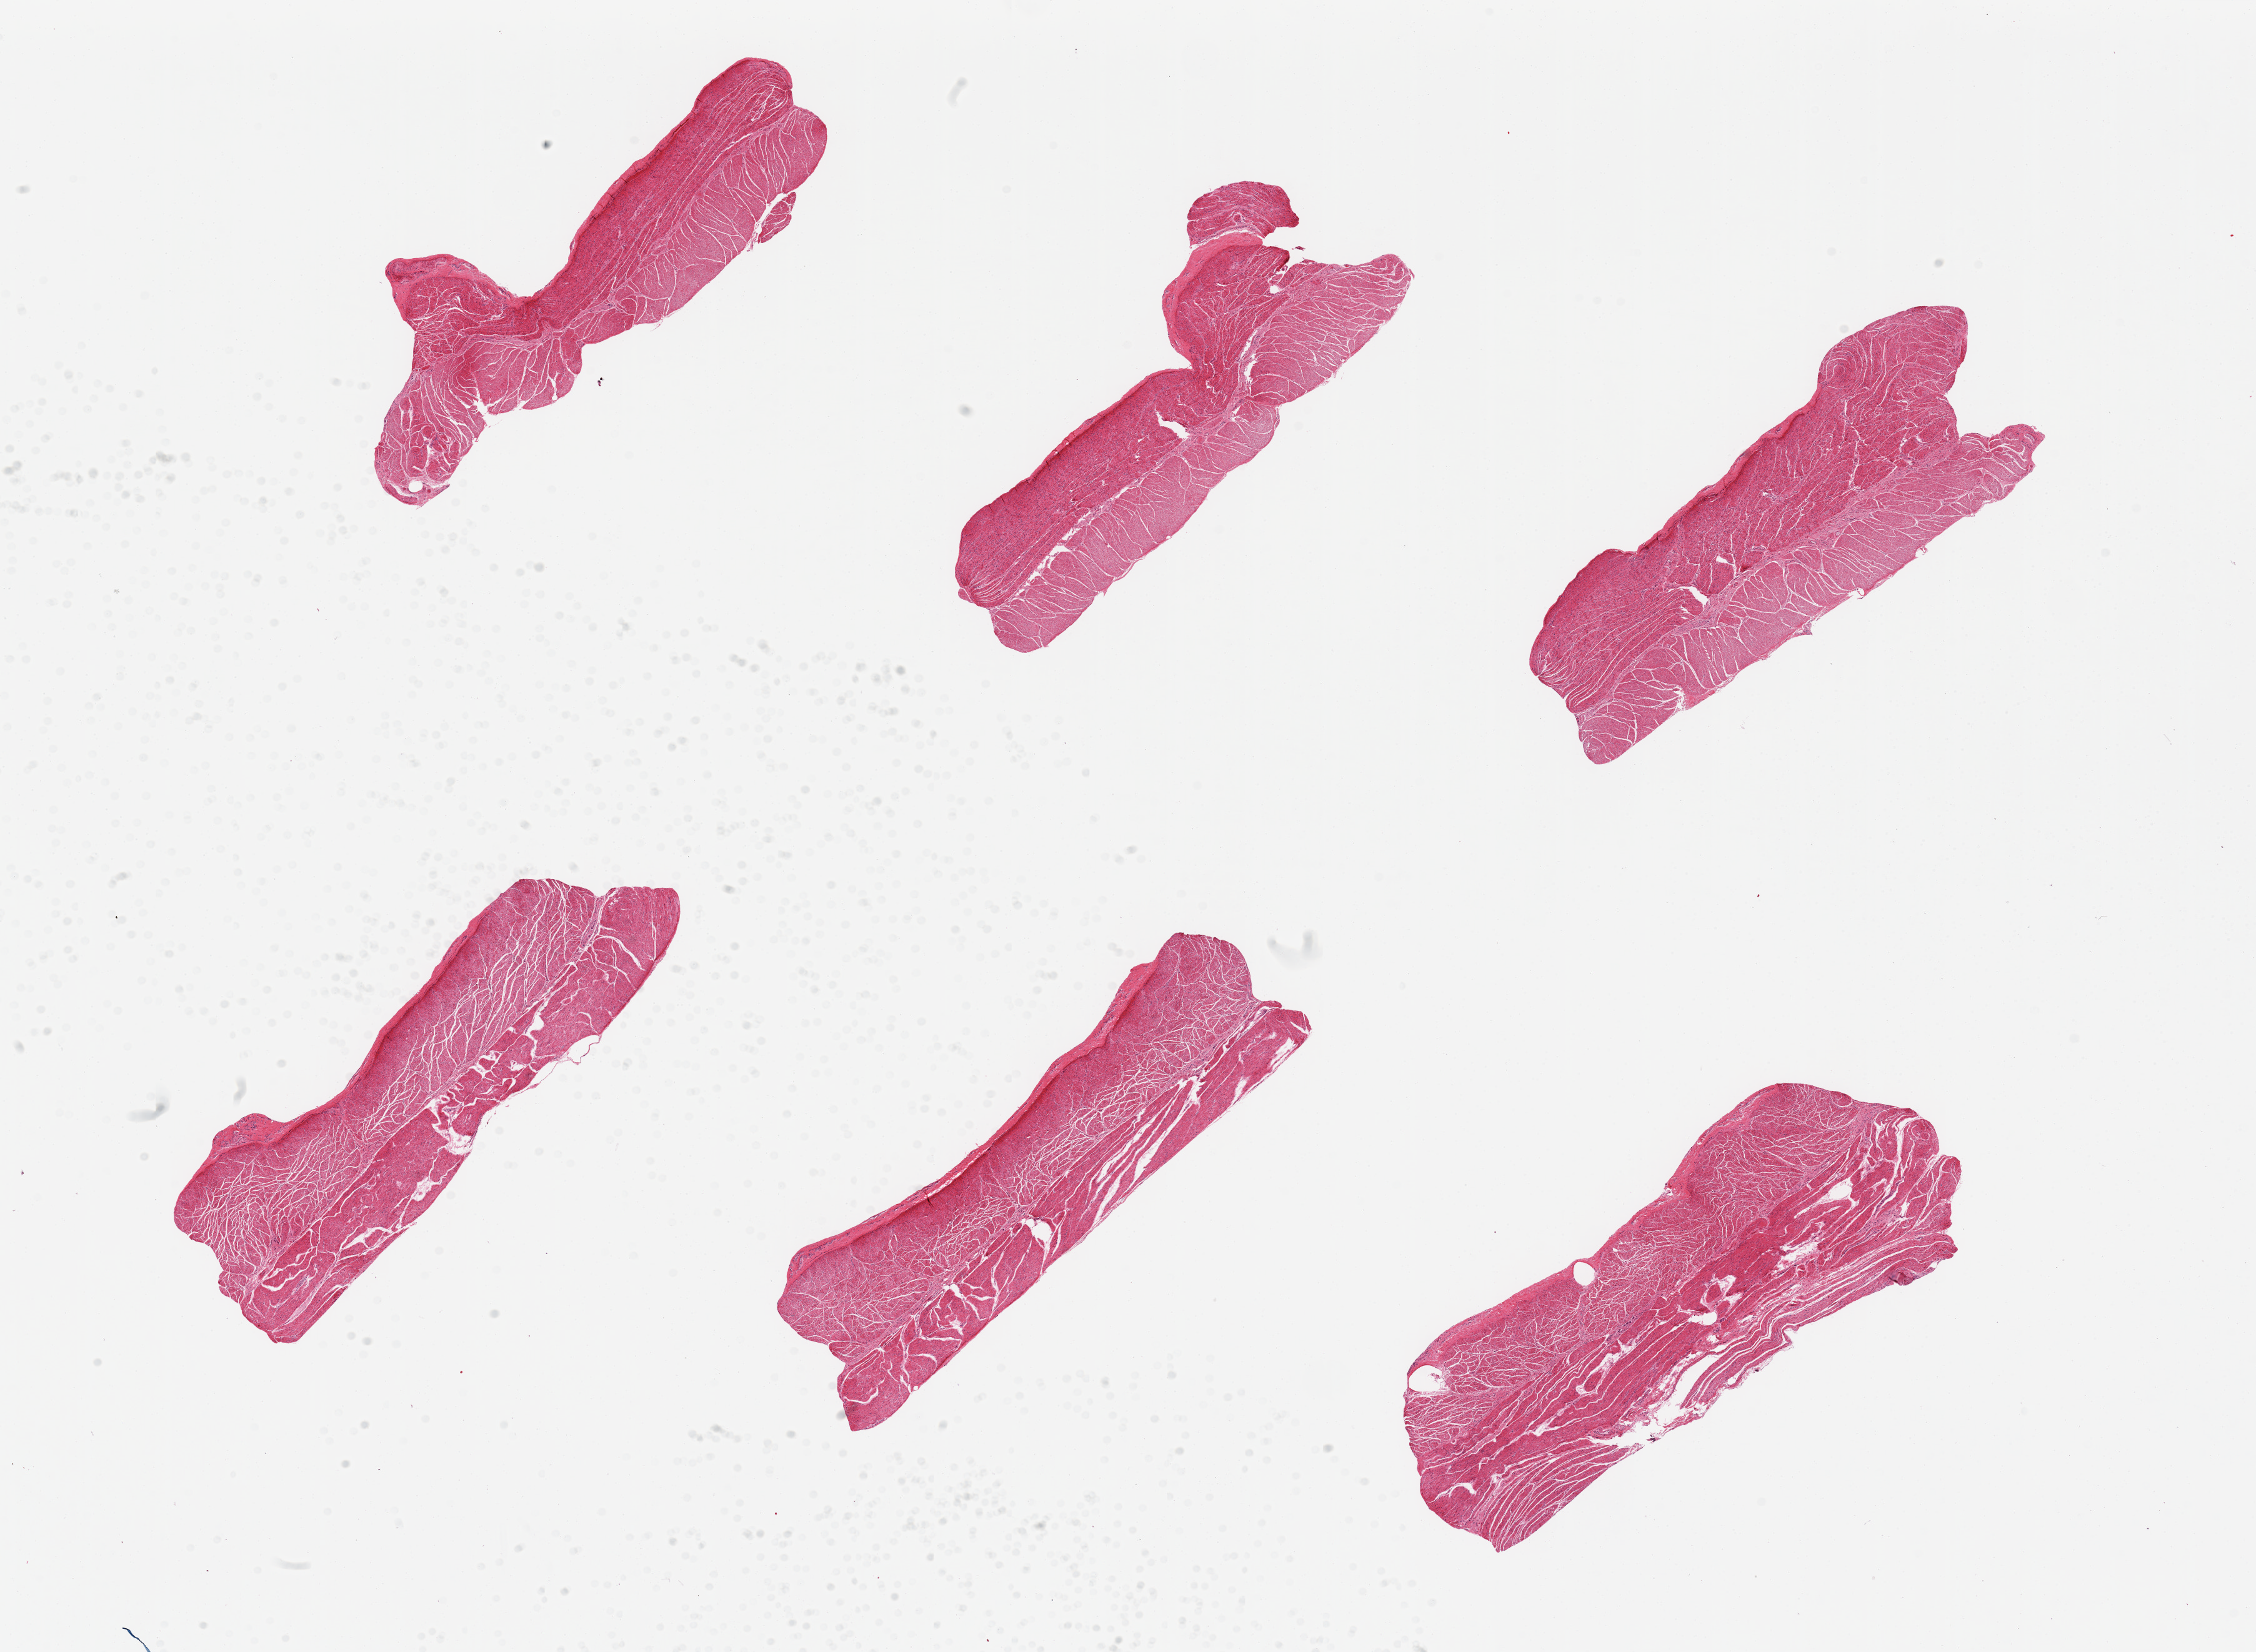
Digitized H&E-stained section — whole scanned area (about 28.5 x 20.9 mm, from a 20x scan) shown as a low-resolution overview, PAXgene-fixed paraffin-embedded (PFPE) section, section of esophageal muscle (target tissue), donor tissue sample. Donor: male.
- reviewer comment on this tissue sample: 6 pieces, all muscularis, good specimens